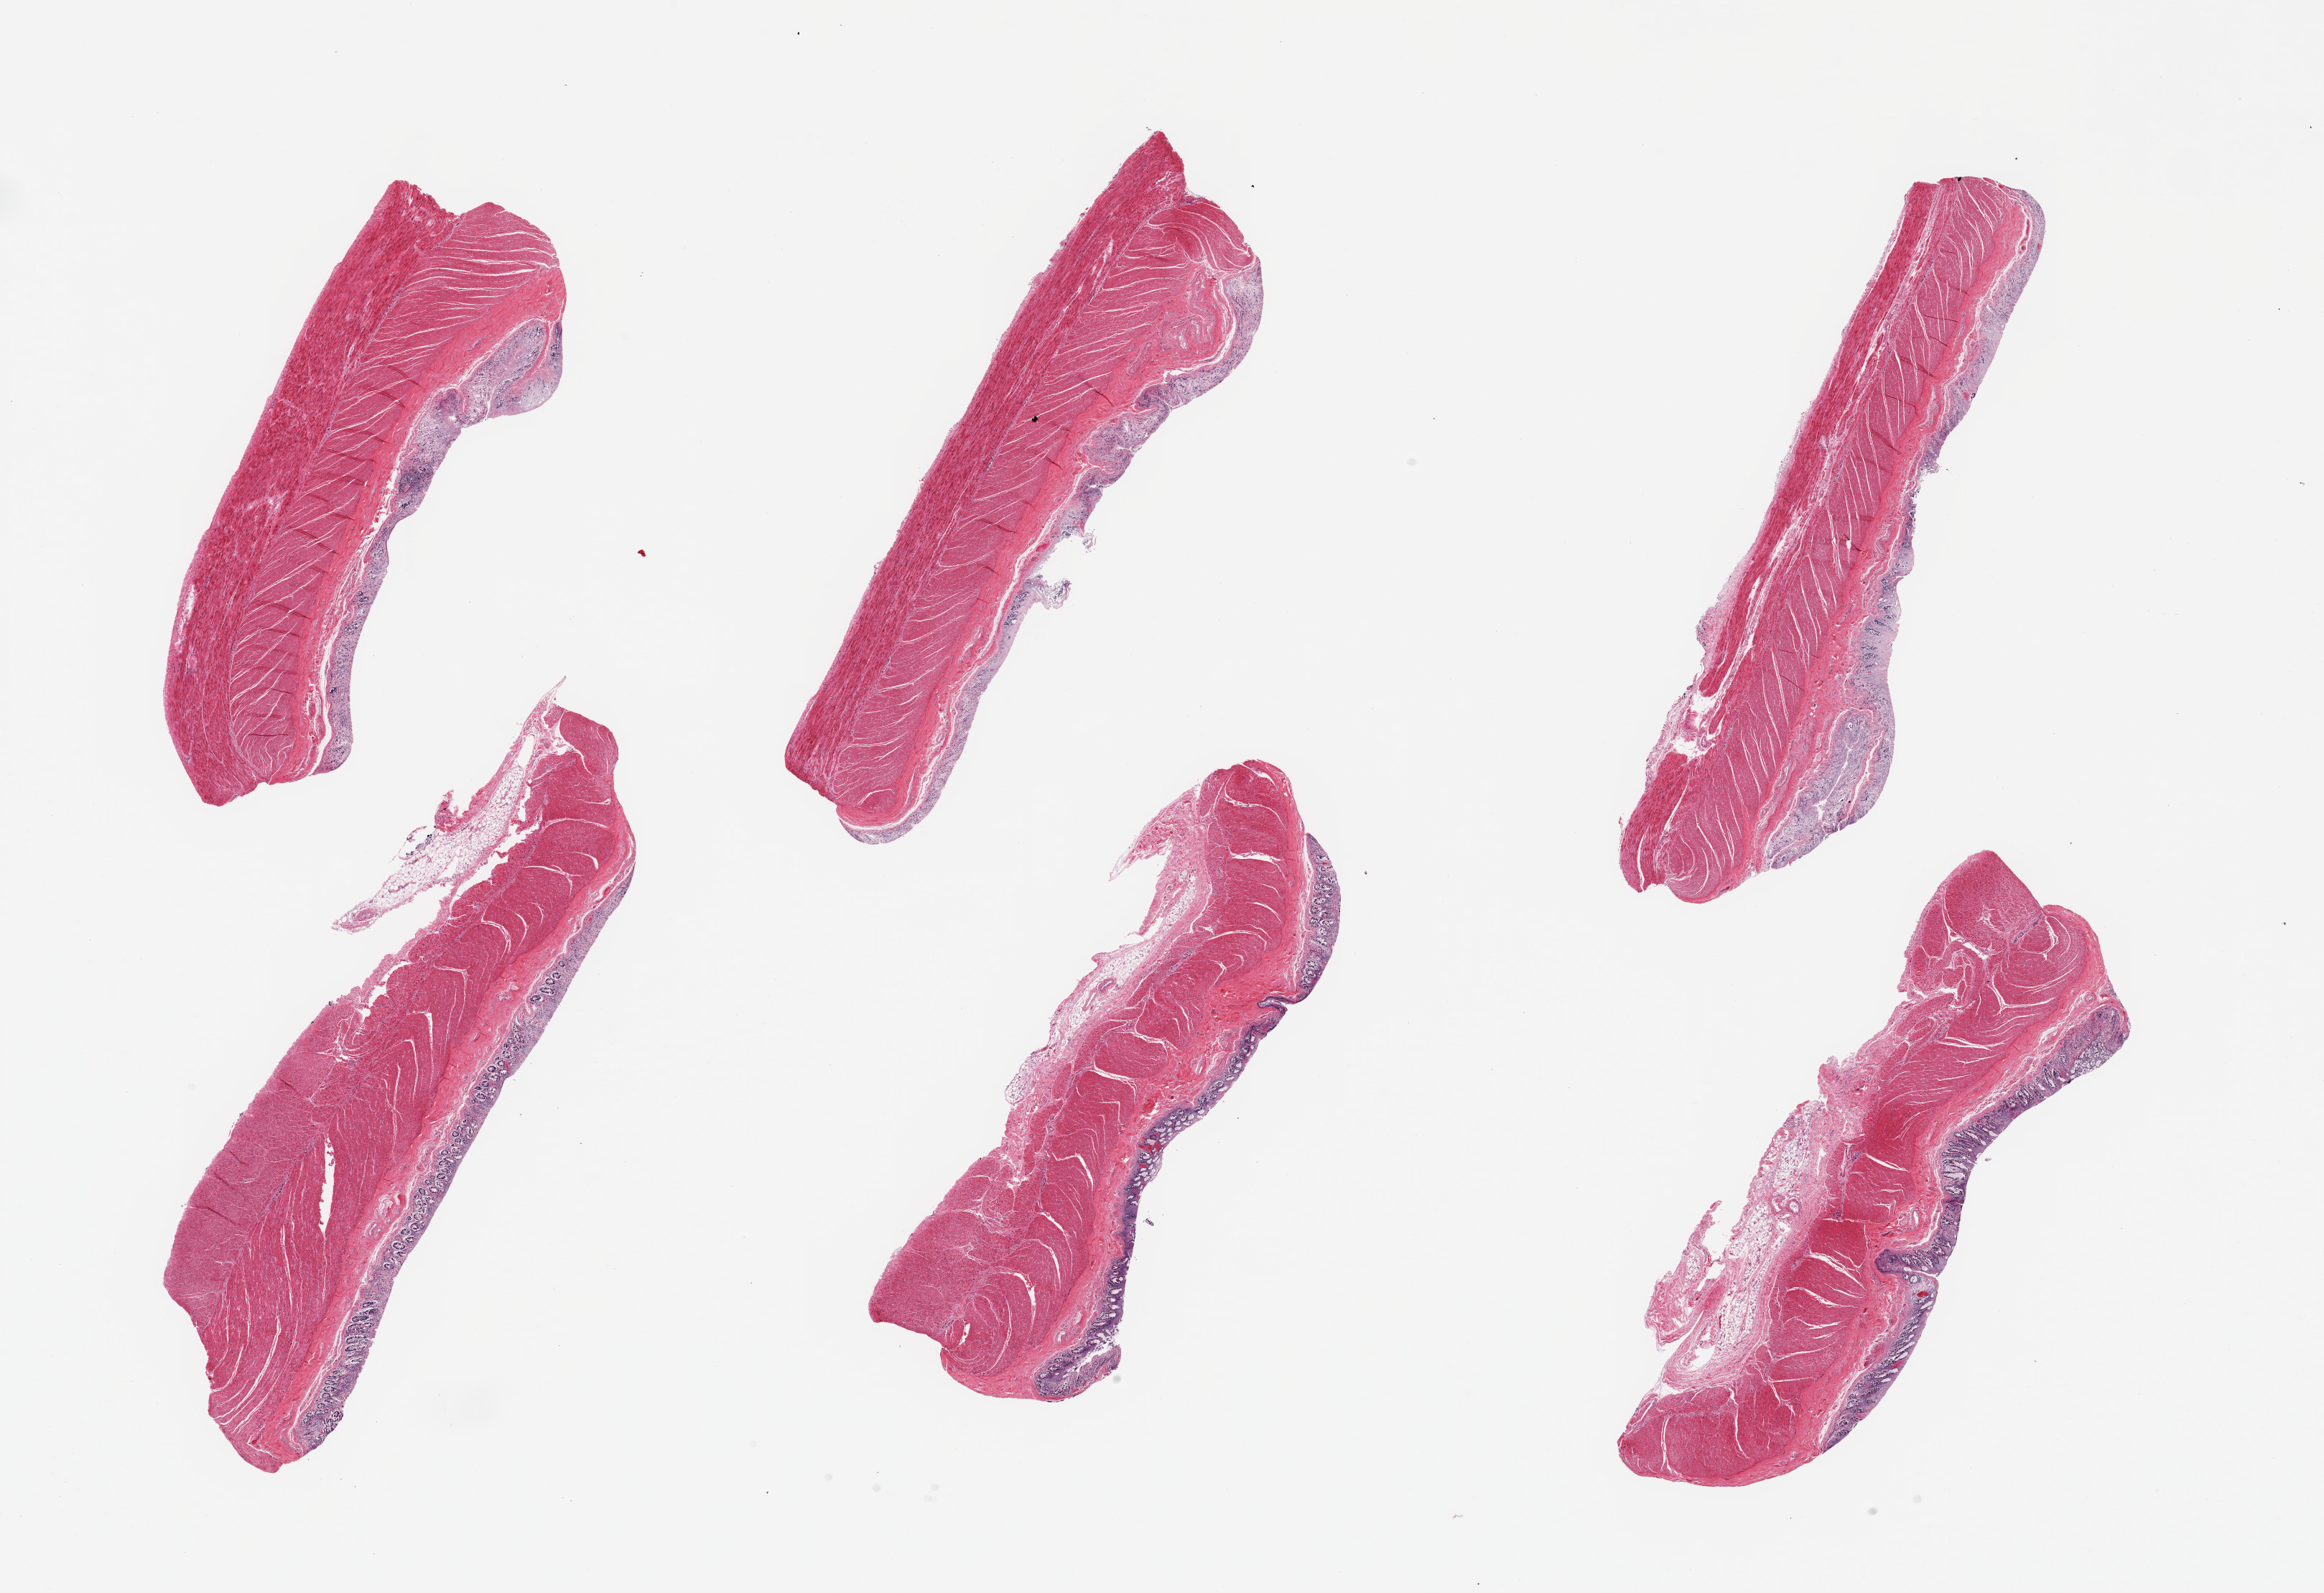
H&E whole-slide image — whole scanned area (about 25.6 x 17.5 mm, acquisition: 20x scan) shown as a low-resolution overview. PAXgene-fixed paraffin-embedded (PFPE) section. Target tissue: transverse colon. Donor tissue sample. Donor sex: male.
* reviewer comment on this tissue sample: 6 pieces; full thickness sections, moderate to severe autolysis of mucosa, few with residual attached fat